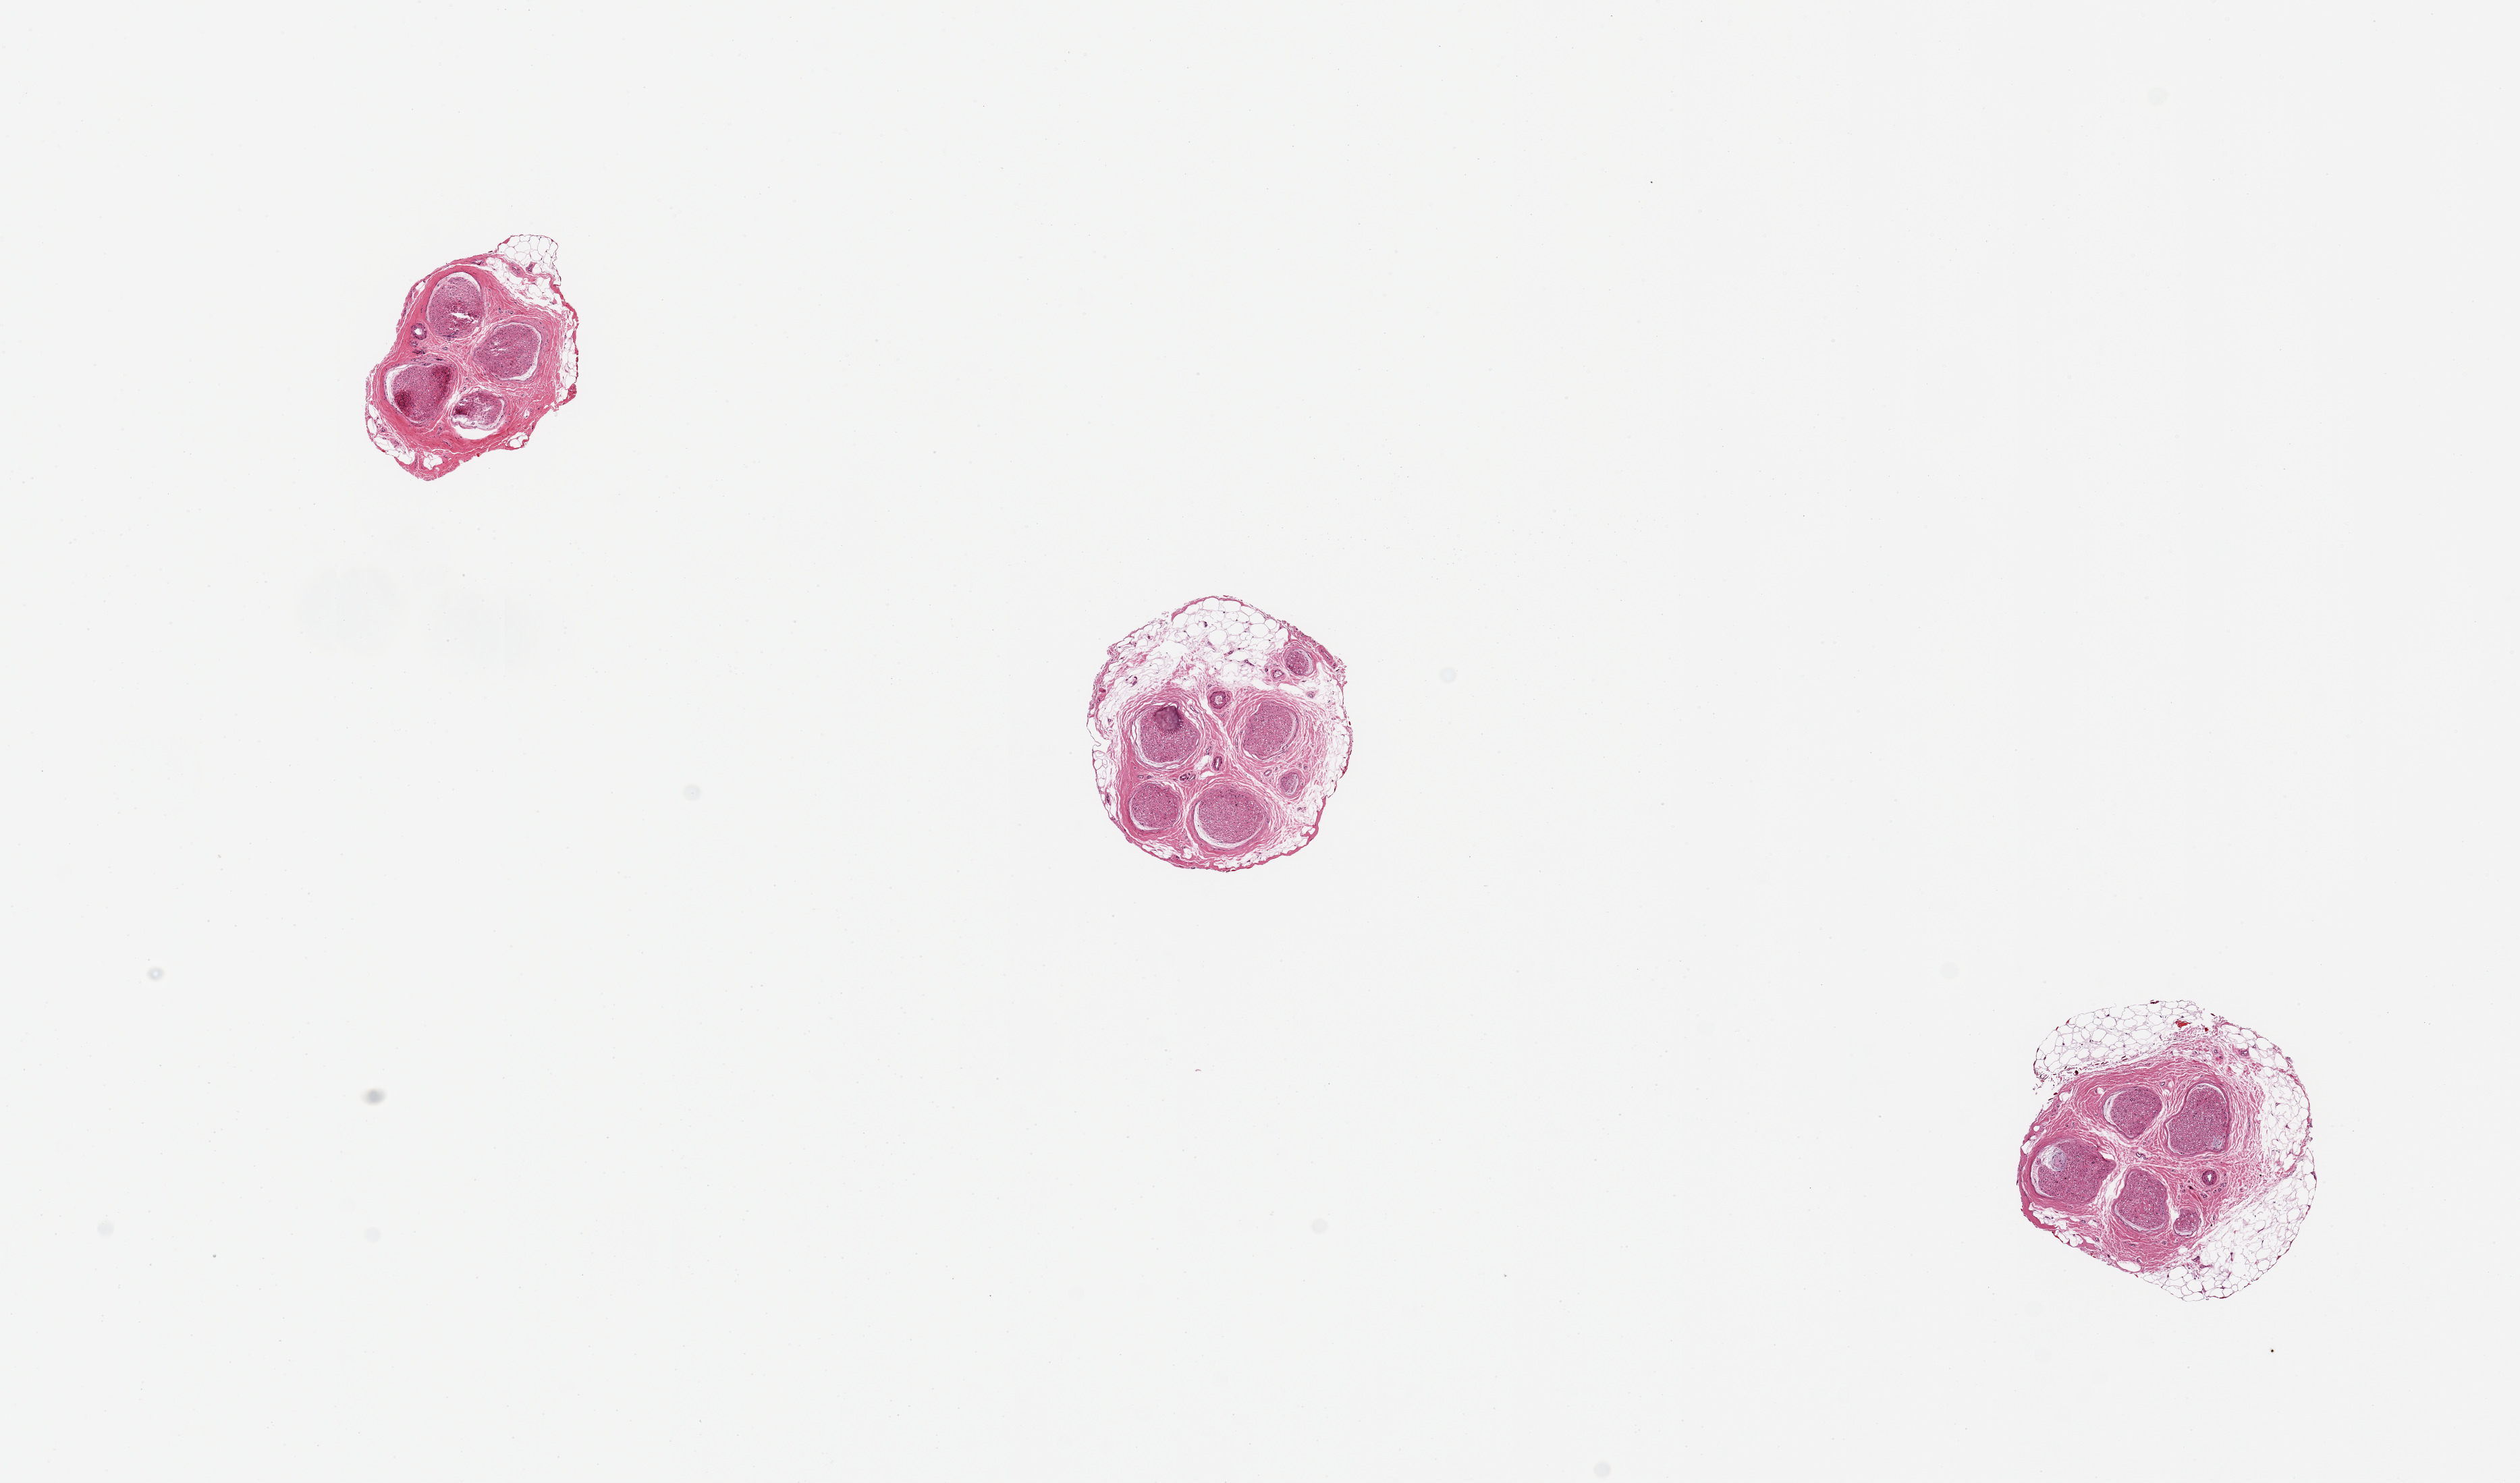
H&E whole-slide image, brightfield, a low-resolution overview of the entire scanned area, about 14.8 x 8.7 mm (slide scanned at 20x). PAXgene-fixed paraffin-embedded (PFPE) section. Section of tibial artery (target tissue). Tissue donor sample. Male donor.
Review note (as recorded): Not artery; 2 ~1.2mm pieces peripheral nerve with 0.5mm rim of fat.